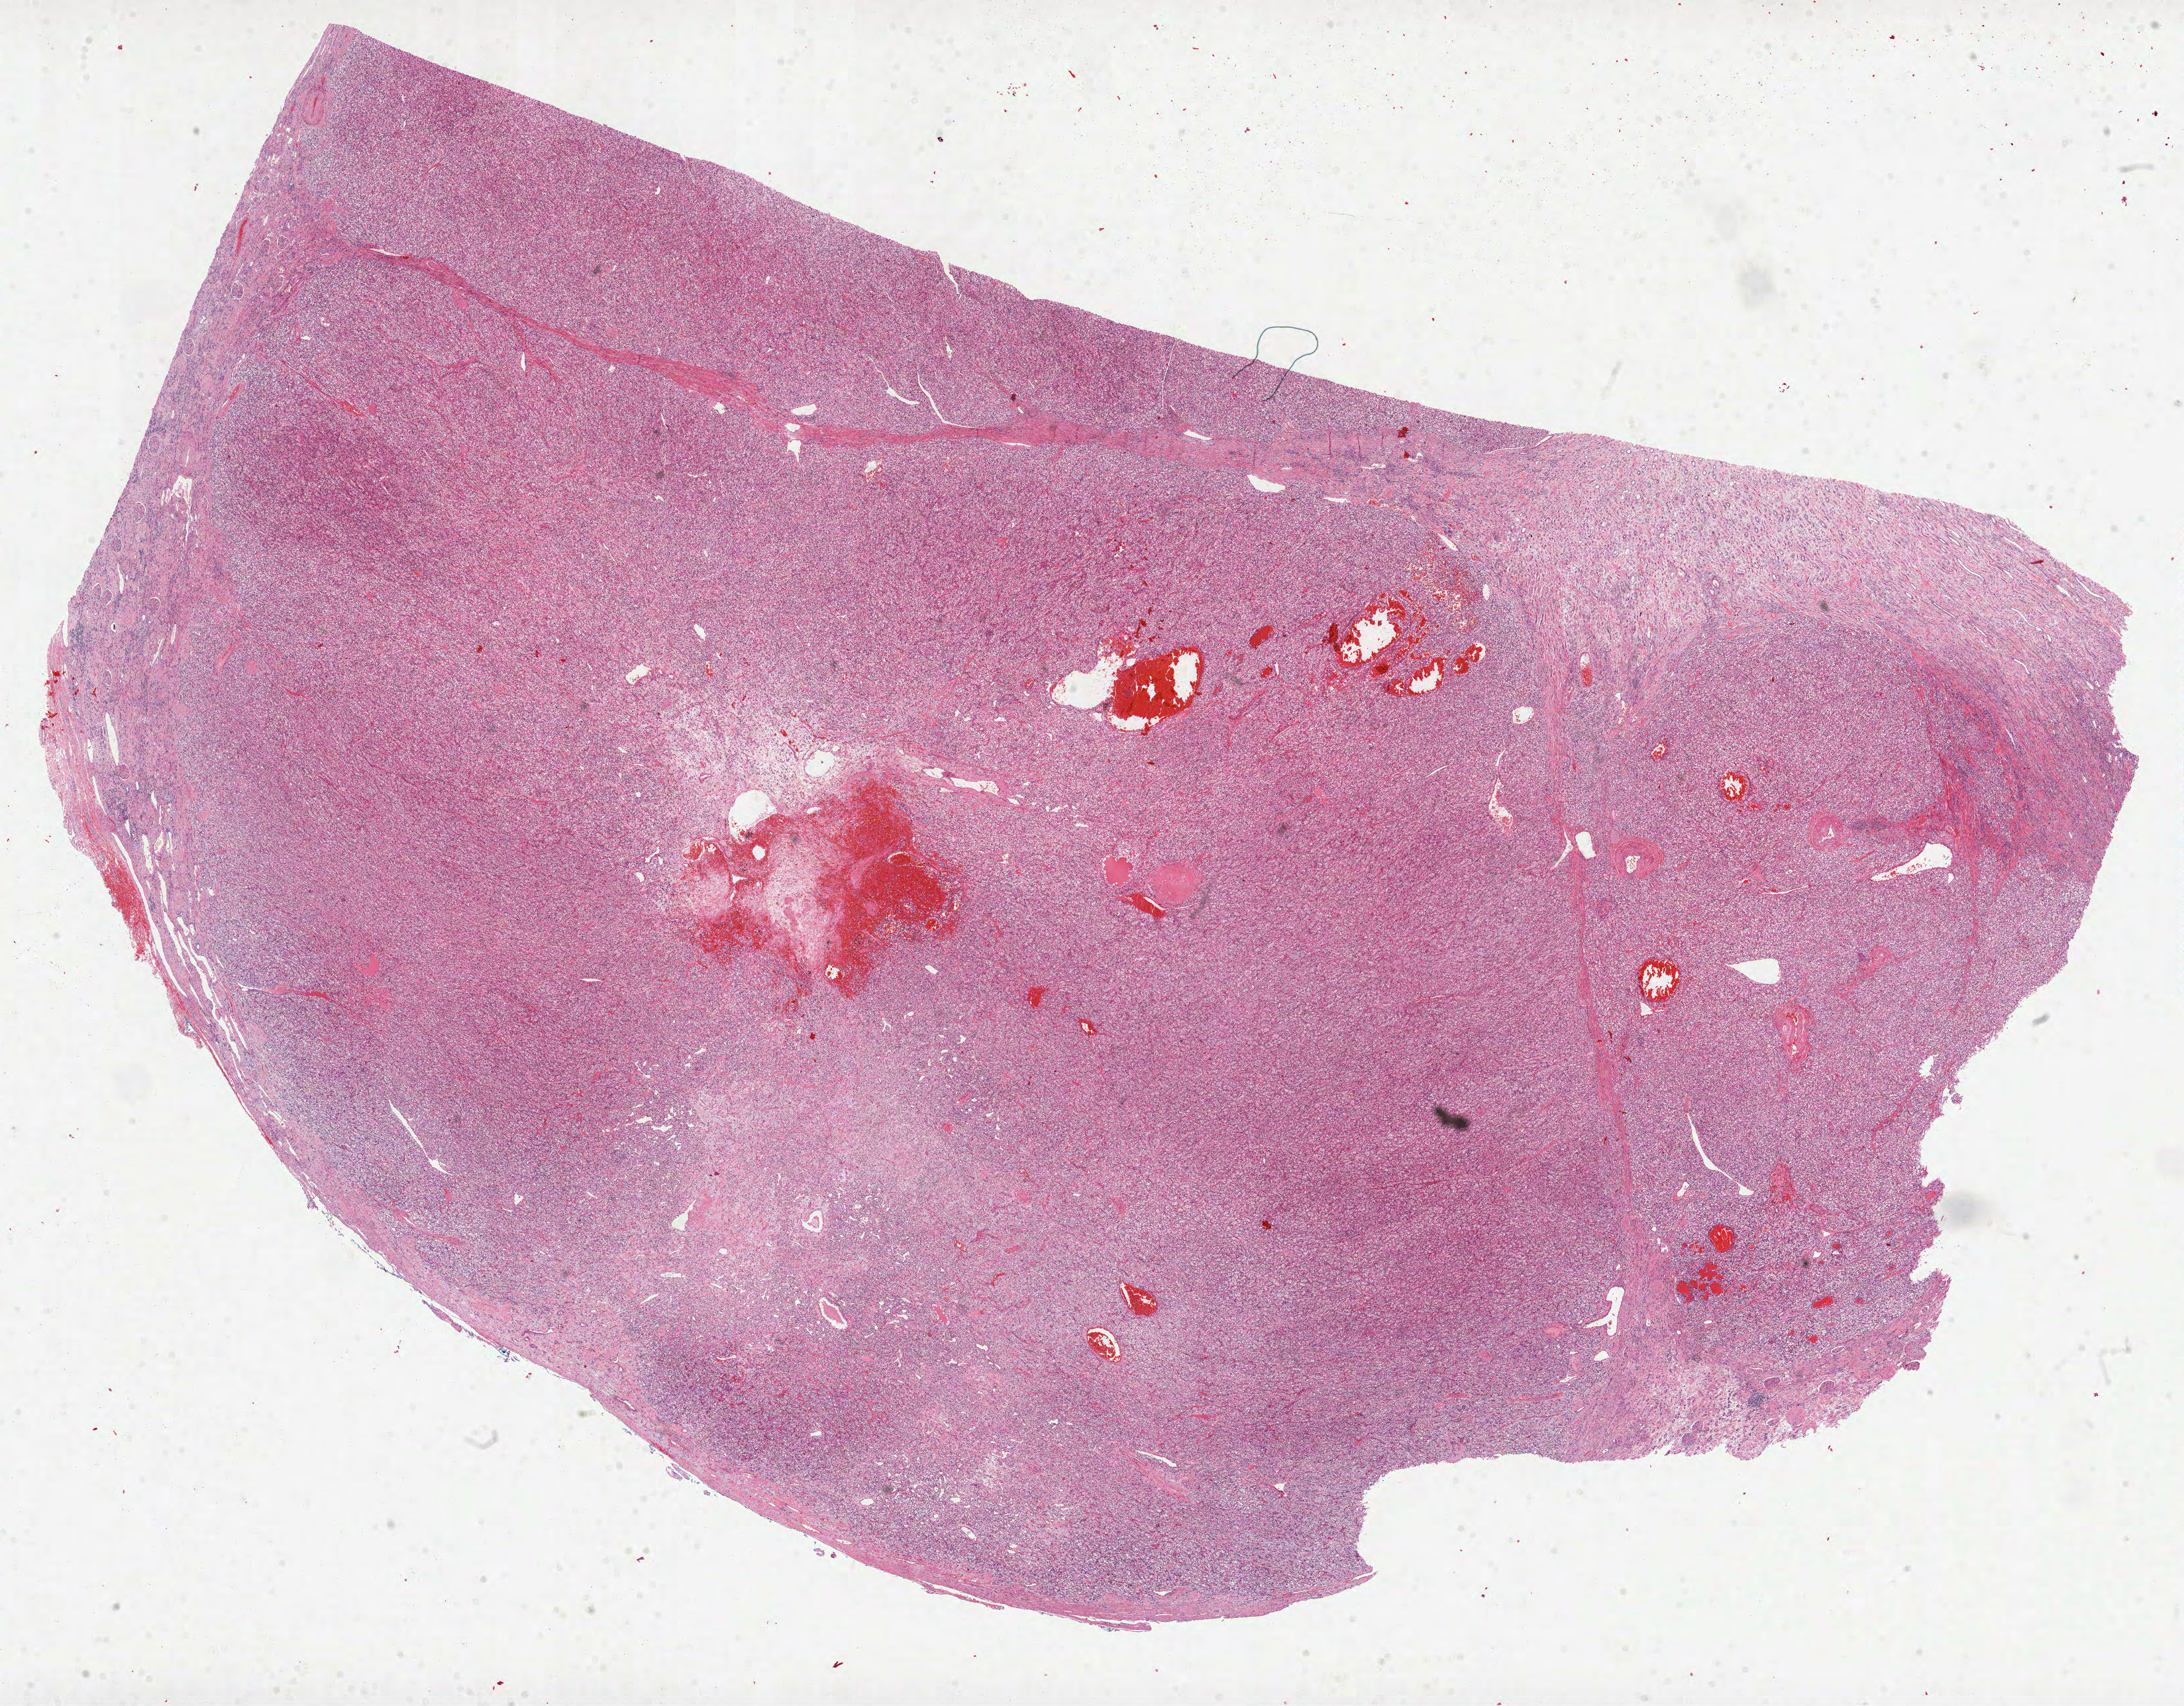
Digitized H&E-stained tissue section (whole slide) — whole scanned area (about 26.6 x 20.8 mm, acquisition: 40x scan) shown as a low-resolution overview; formalin-fixed paraffin-embedded (FFPE) diagnostic section; sample: primary tumour, kidney. Patient: male, age at initial diagnosis 68 years.
Histologic diagnosis: Clear cell adenocarcinoma, NOS.